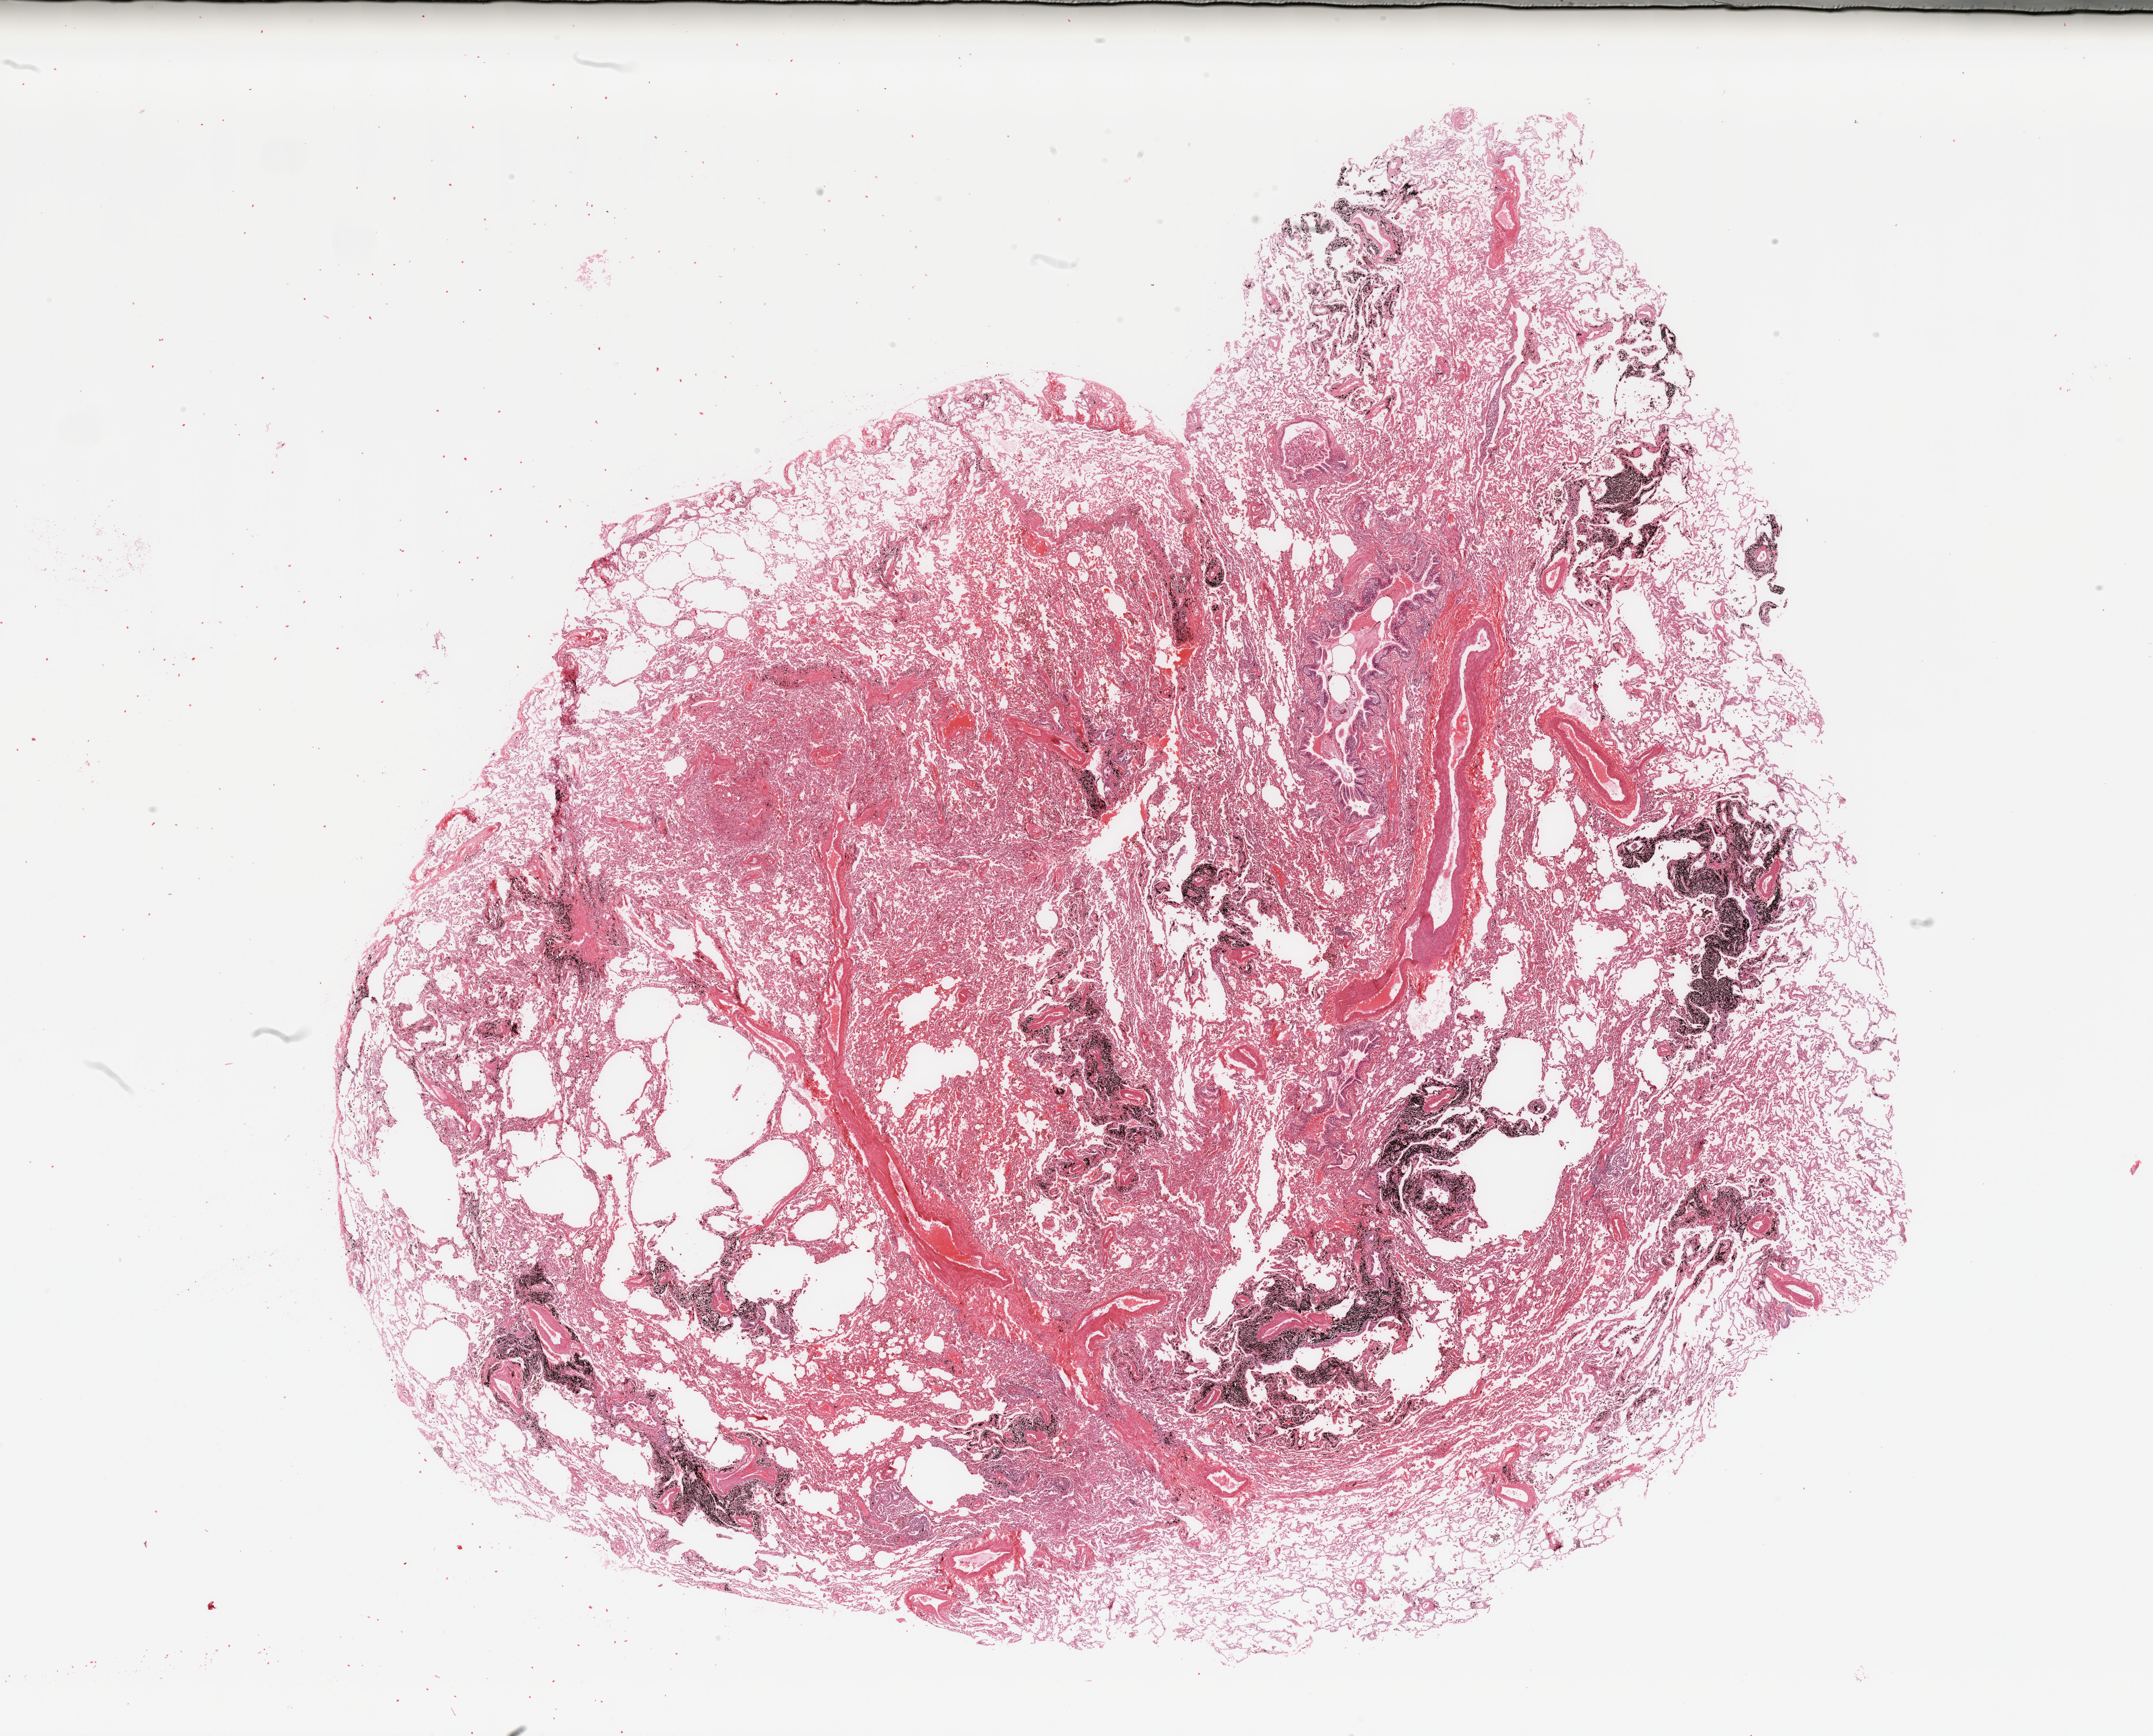
Whole-slide histology image, Hematoxylin and eosin (H&E) stained — whole scanned area (about 29.5 x 23.8 mm, from a 20x scan) shown as a low-resolution overview, normal (non-tumour) tissue sample, sampled site: lung. Patient: male, age 63 years.
- this section: normal (non-tumour) tissue from the same patient
- patient diagnosis: Adenocarcinoma, NOS